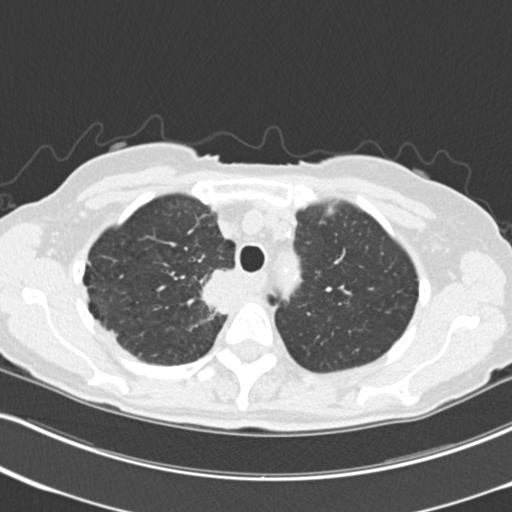
Low-dose screening chest CT, axial slice. Third annual screen. Lung window (W 1500 / L -600 HU). Slice 49 of 226 in the series. Female, age 68 years at enrolment. Current smoker at enrolment.
Expert reader's lesion annotation, bounding box (x1, y1, x2, y2) in pixels: (199, 264, 251, 319). Reader record for this screening exam (exam-level; its link to the box is not recorded): non-calcified nodule or mass ≥4 mm, right upper lobe, 31 × 29 mm, poorly defined margins, soft tissue attenuation, pre-existing on the prior screen: no. Official screen result: positive, other. Lung cancer was diagnosed 79 days after this screen: squamous cell carcinoma, NOS, right upper lobe, mediastinum, poorly differentiated (G3), stage IIIB (AJCC 6th edition), 43 mm at pathology.